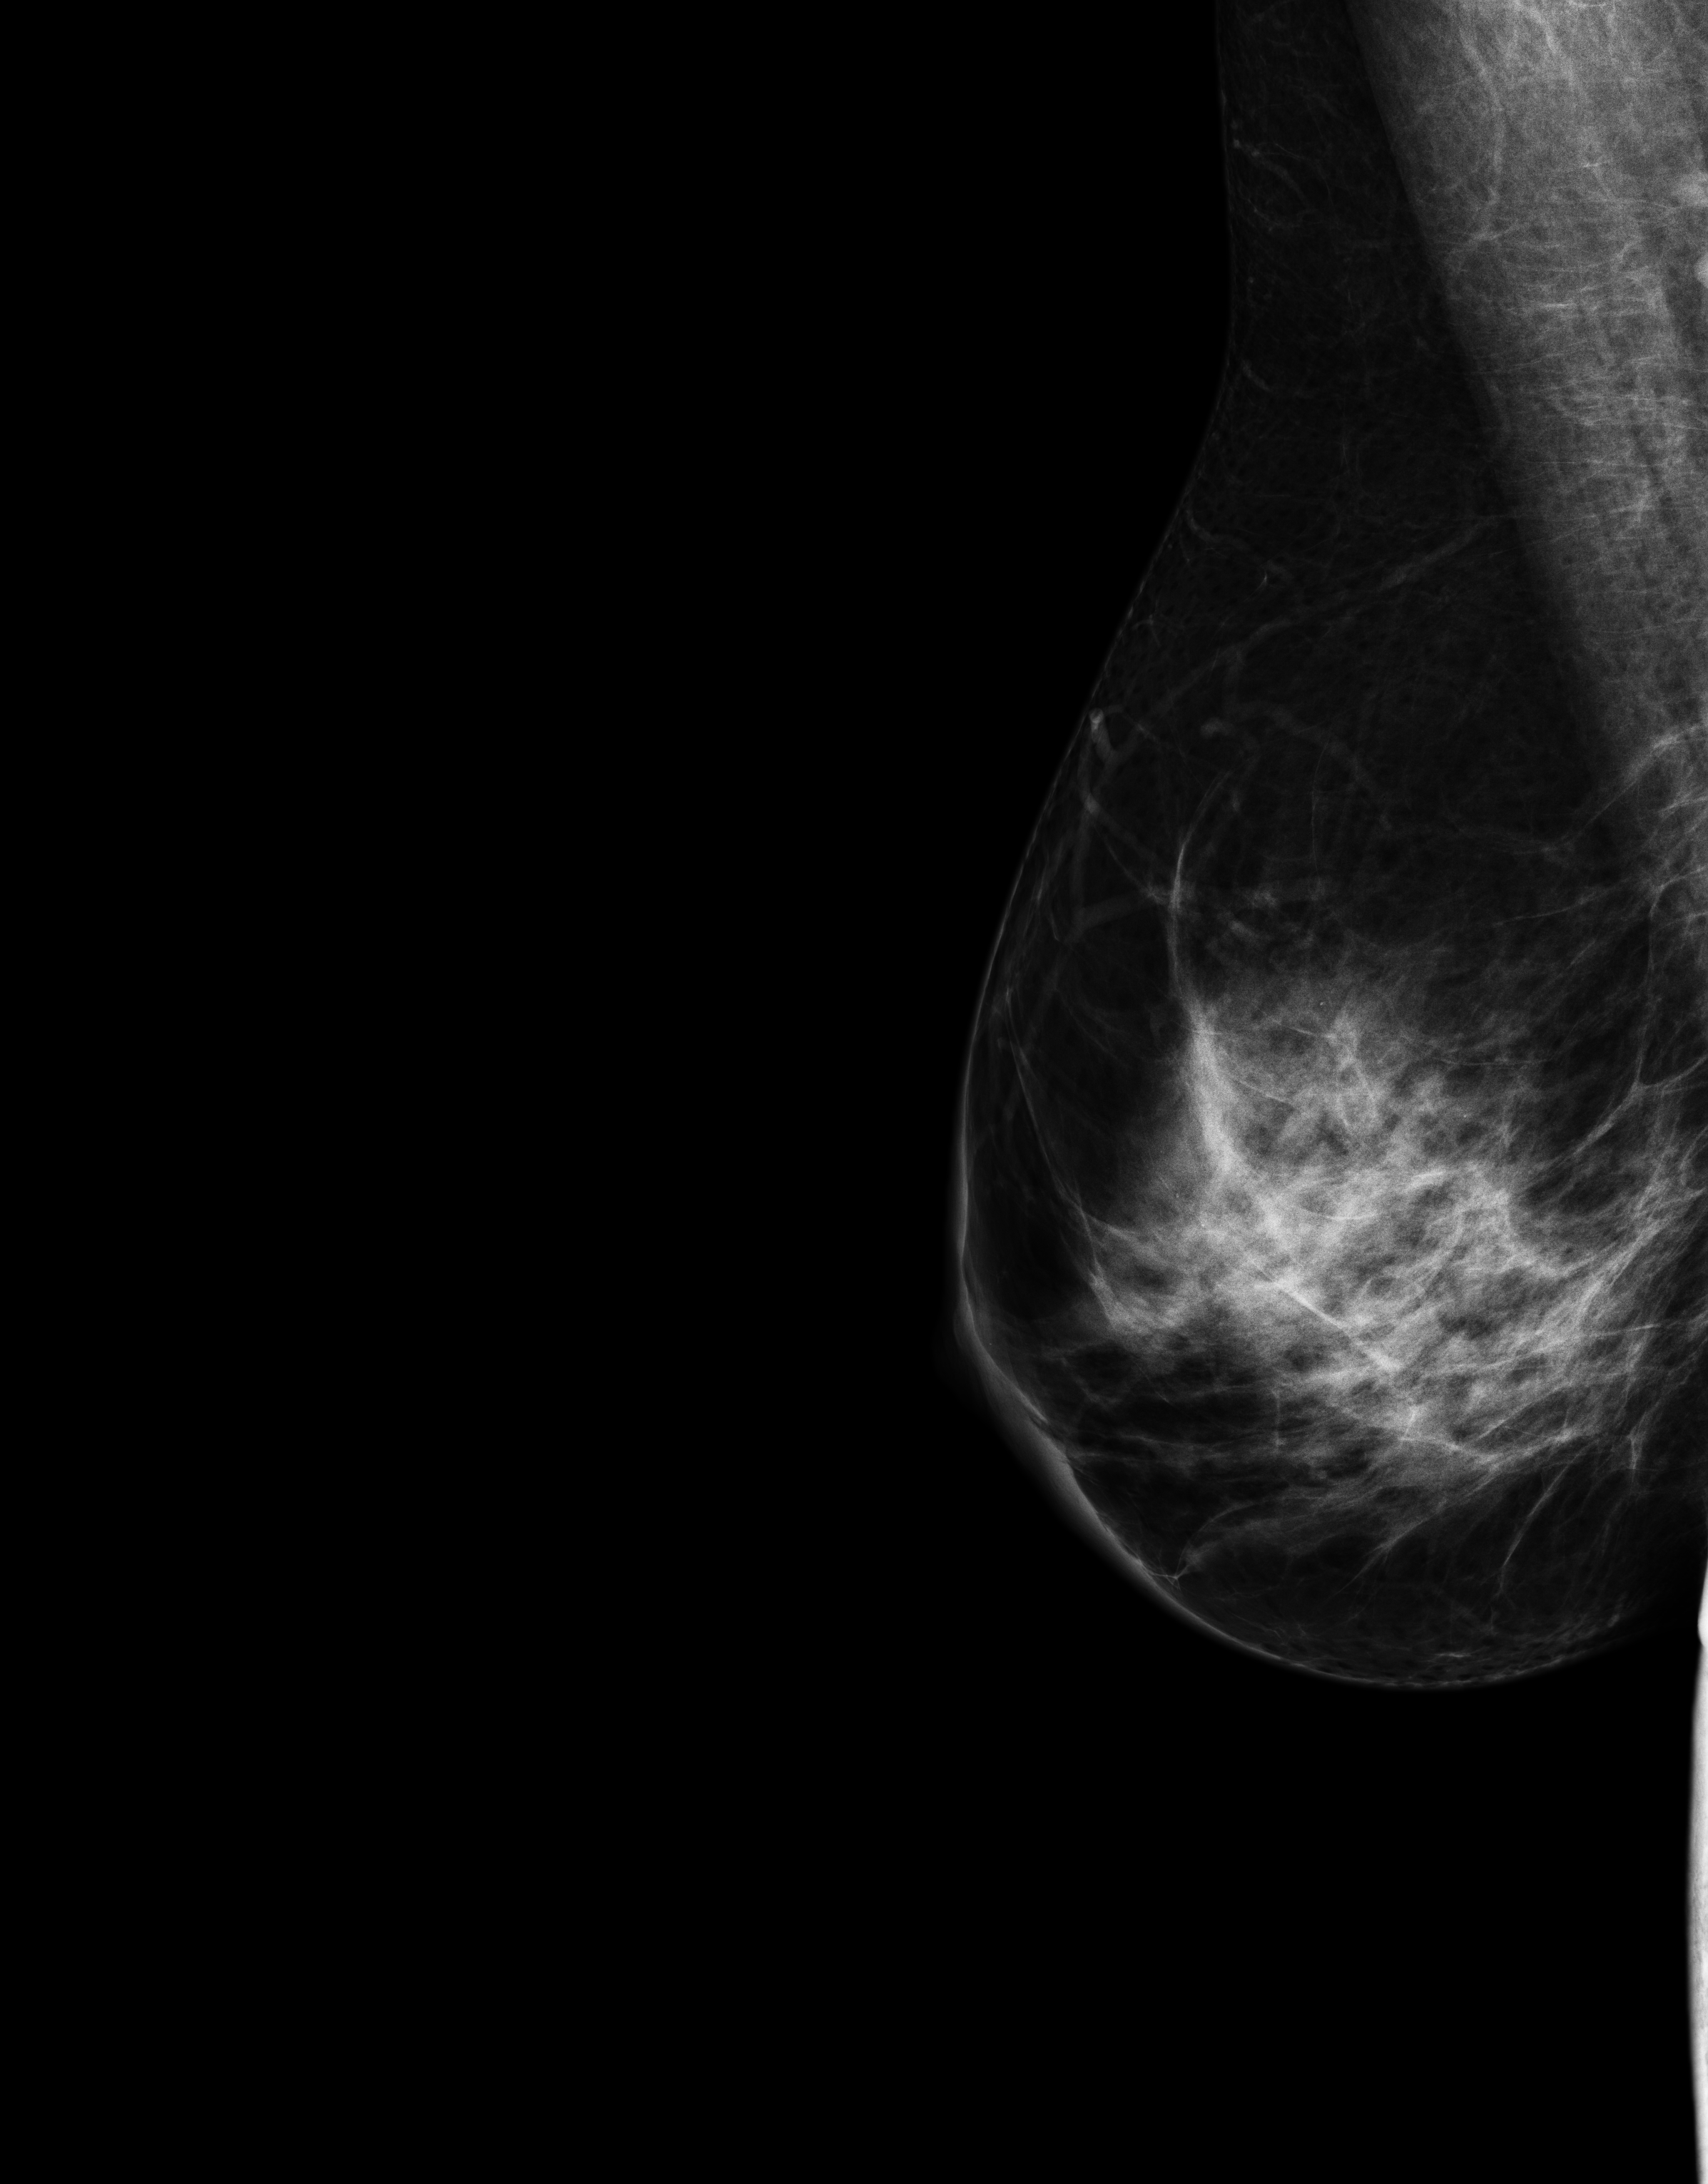
Full-field digital mammogram (FFDM); right breast; MLO view; annual screening mammography examination. Patient aged 44 years (female).
Final BI-RADS category for the screening round (tomosynthesis exam, both breasts): category 1.